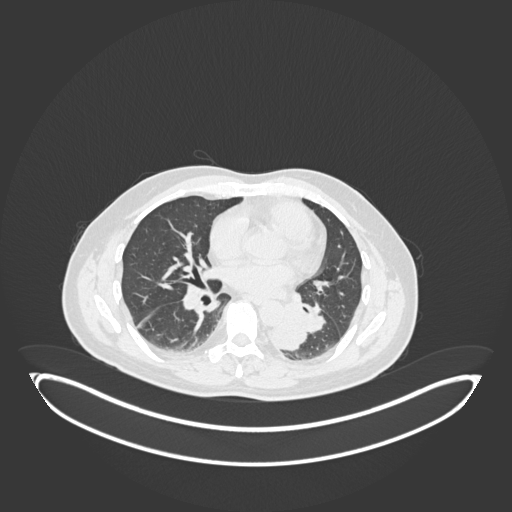
Chest CT, one axial slice. Slice 90 of 258 in the series (ordered by position). Reconstruction kernel B30f. 120 kVp. Lung window (W 1500 / L -600 HU). 512 × 512 image matrix, field of view 500 × 500 mm. Patient: male, 54 years. From the clinical record (not read from this slice): clinical TNM (as recorded): T3 N0 M0.
Outlined on this slice (rectangle marked by the reading radiologist):
- lung tumour (recorded histology: squamous cell carcinoma): bounding box (x1, y1, x2, y2) in pixels: (267, 298, 307, 354)